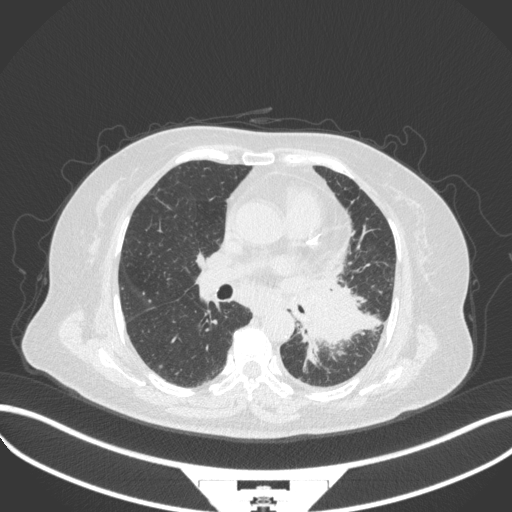
Chest CT, one axial slice; slice 184 of 328 in the series (ordered by position); reconstruction kernel B31f; 120 kVp; lung window (W 1500 / L -600 HU); 1 mm slice thickness; 512 × 512 image matrix, field of view 400 × 400 mm. Female patient, age 69 years. From the clinical record (not read from this slice): clinical TNM (as recorded): T2b N3 M1.
Outlined on this slice (rectangle marked by the reading radiologist):
- lung tumour (recorded histology: adenocarcinoma): bounding box <301,286,369,356> (left, top, right, bottom; pixels)